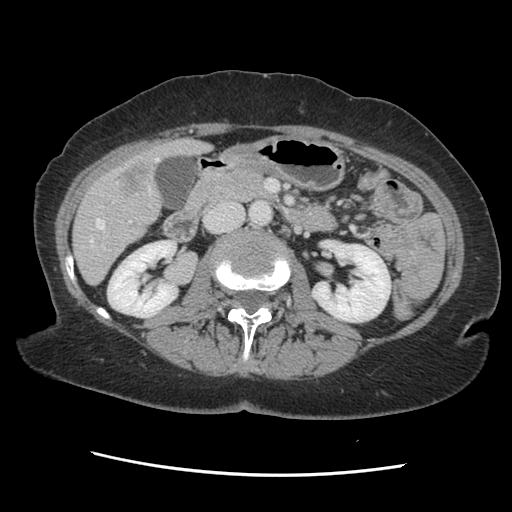
Contrast-enhanced abdominal CT, one axial slice. Slice 58 of 141 in the series (ordered by position). Soft-tissue window (W 400 / L 40 HU). 512 × 512 image matrix, field of view 330 × 330 mm. Female patient, age 61 years. Case-level facts recorded for this patient, not image findings: diagnosis: colorectal cancer liver metastases, imaged before liver resection; multiple liver metastases: no; largest metastasis: 2.4 cm; disease in both lobes: no.
Outlined on this slice (expert manual segmentation):
- hepatic veins: bounding box (x1, y1, x2, y2) in pixels: (90, 157, 159, 246)
- liver: (74, 140, 208, 283)
- planned liver remnant (the part of the liver to remain after resection): (74, 193, 160, 283)
- portal vein (with intrahepatic branches): (102, 182, 131, 246)
- liver metastasis: (117, 161, 154, 195)